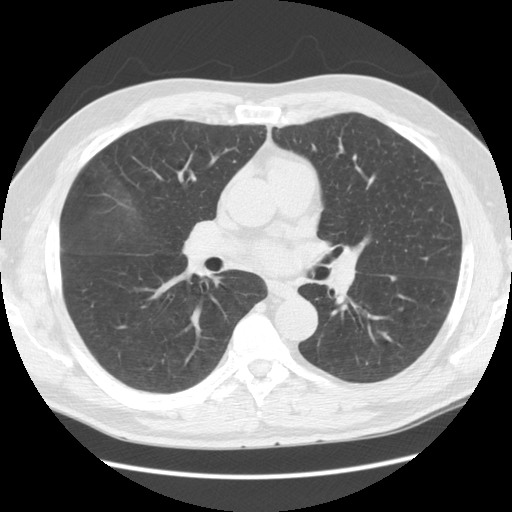
Chest CT (low-dose screening protocol), one axial image. Second annual screen. Lung window (W 1500 / L -600 HU). 2.5 mm slice thickness. Male participant, aged 60 years at enrolment. Current smoker at enrolment.
Expert reader's lesion annotation, box from (x=385, y=297) to (x=417, y=325) px. The screening reader recorded 4 non-calcified nodules or masses ≥4 mm on this exam; which of them this box marks is not recorded. Lung cancer was diagnosed 594 days after this screen: large cell neuroendocrine carcinoma, left lower lobe, poorly differentiated (G3), stage IB (AJCC 6th edition), 33 mm at pathology.